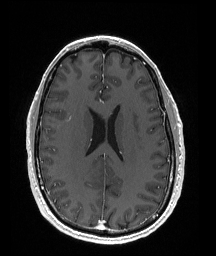
Brain MRI from a brain-tumour surgery series, one axial slice; position 73 of 176 along the scan axis; T1-weighted post-contrast; 216 × 256 image matrix. From the clinical record (not read from this slice): histopathology: Oligodendroglioma; WHO grade: 2; IDH mutation: yes; tumour location: Right Parietal.
Outlined on this slice (outlined manually by an expert reader):
- tumour: bounding box [x1, y1, x2, y2] px = [91, 180, 103, 189]